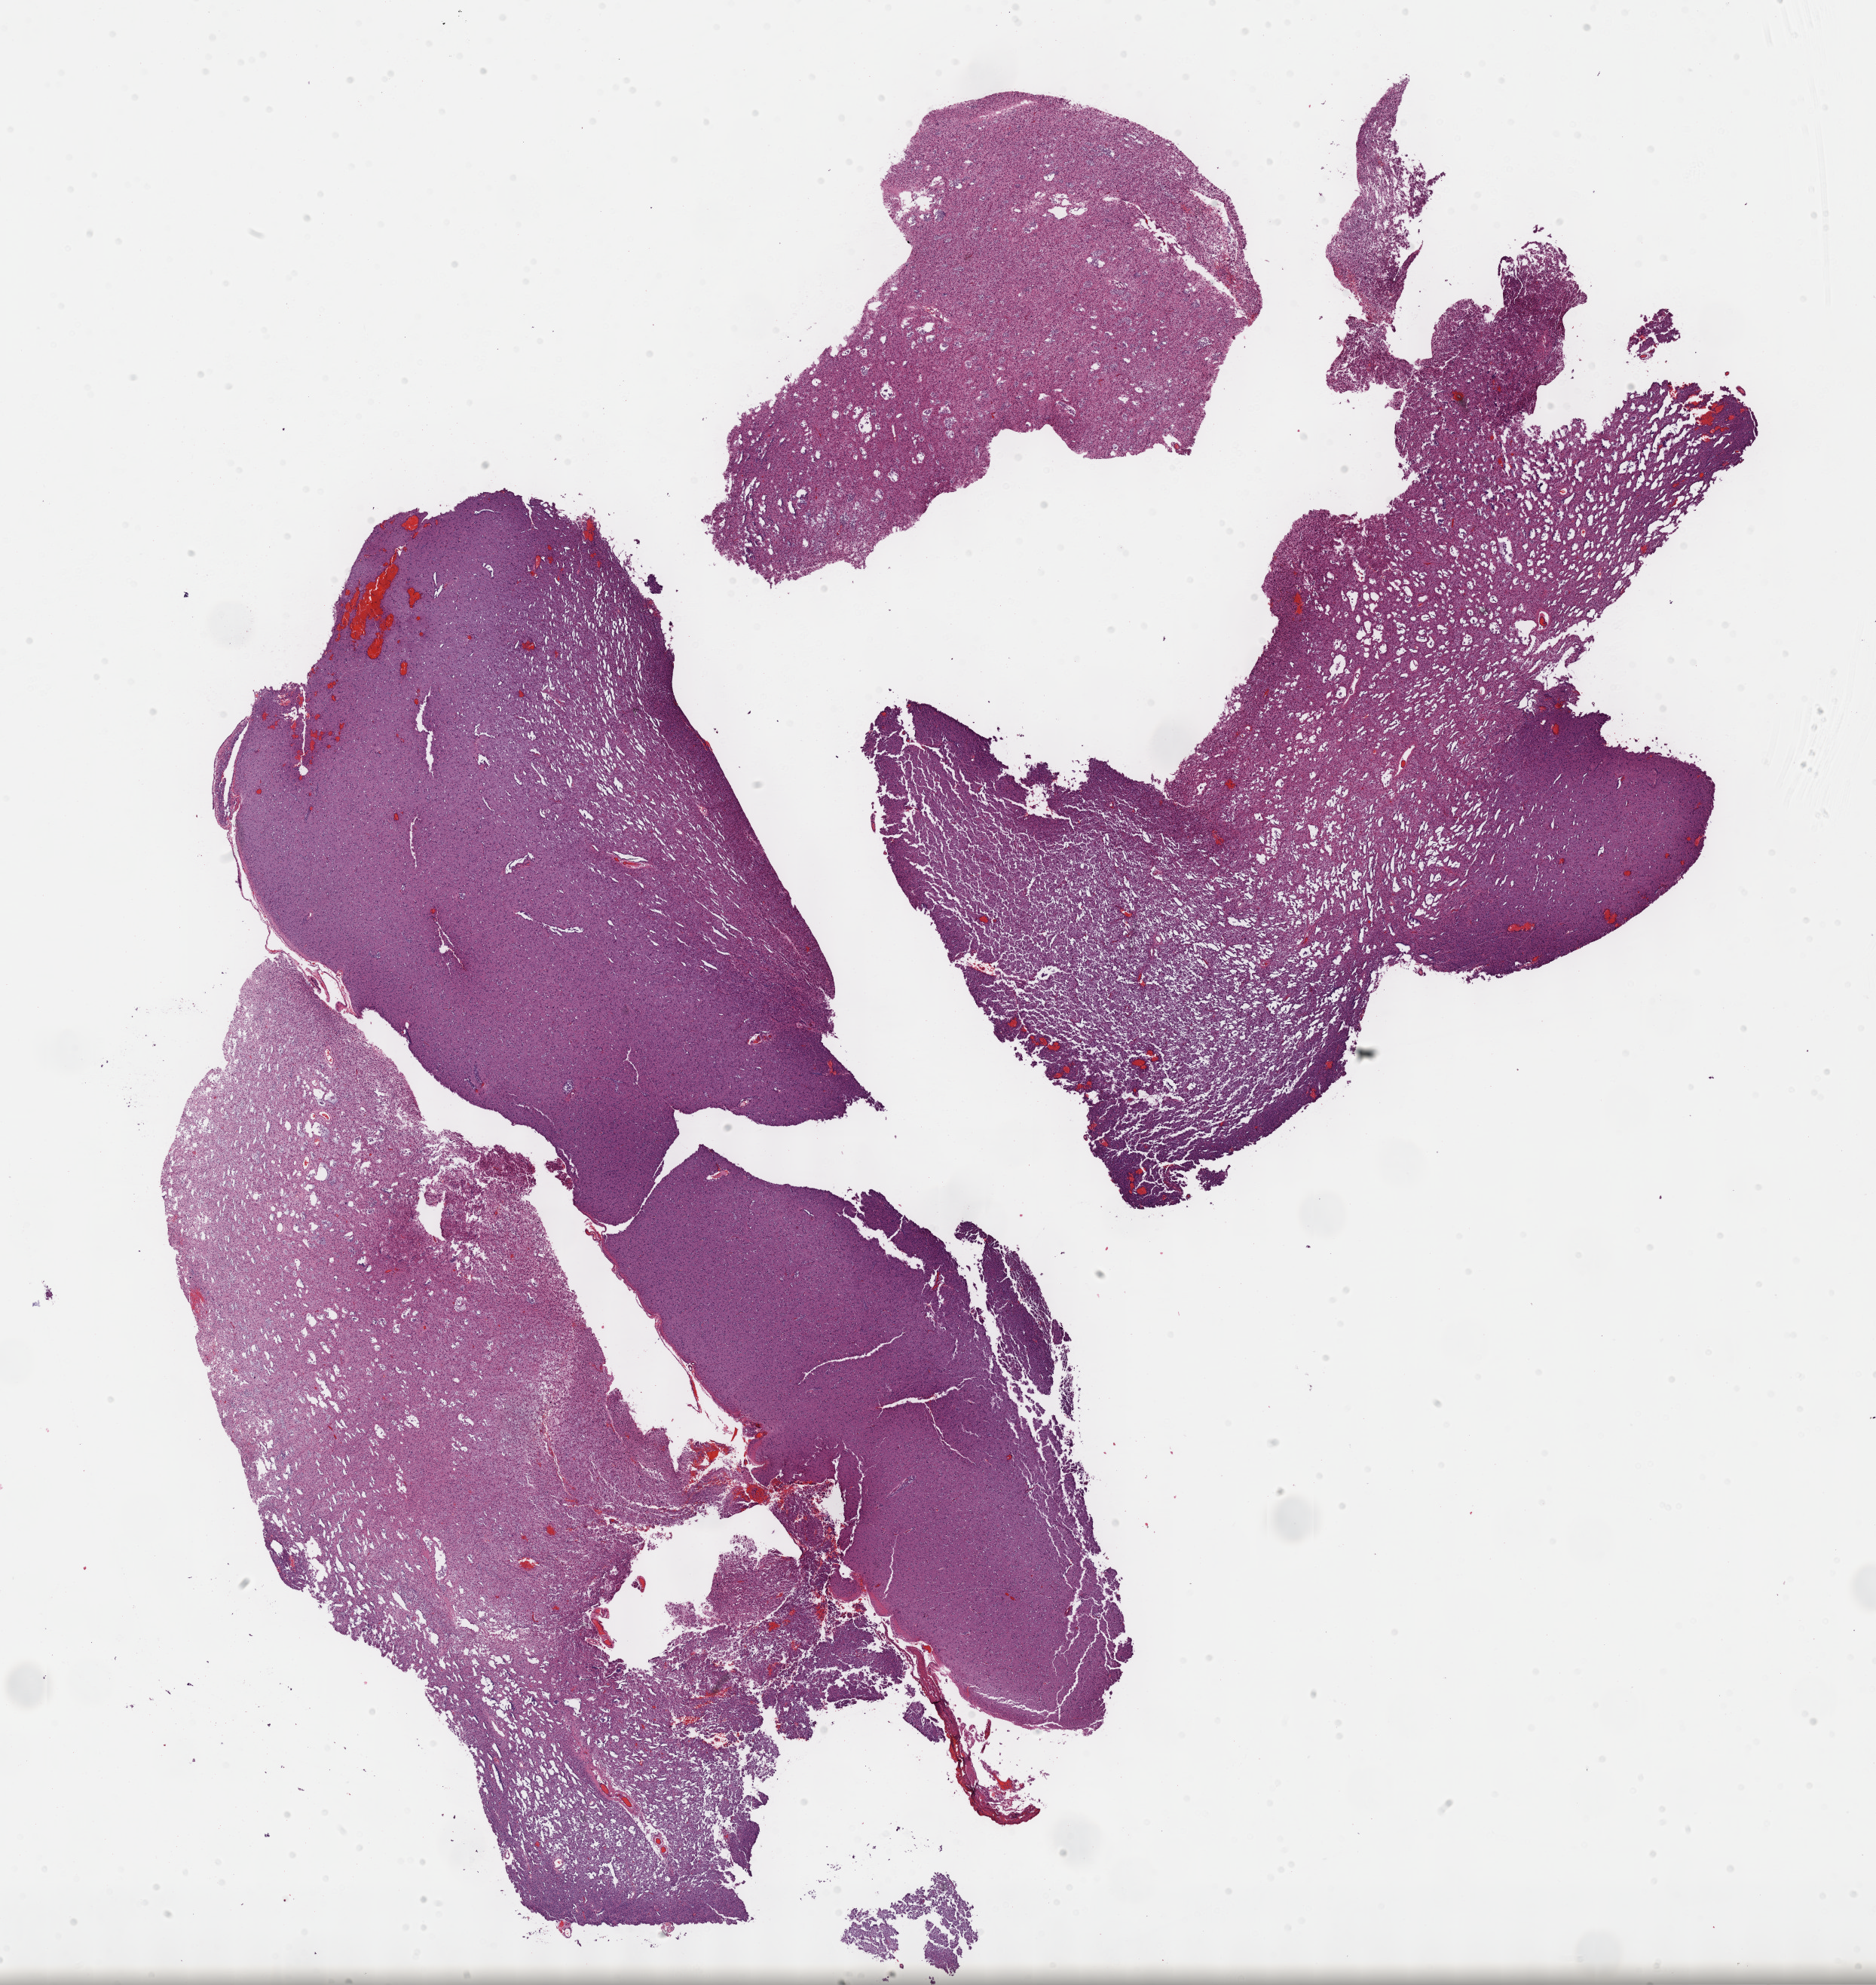
Whole-slide histology image, Hematoxylin and eosin (H&E) stained — whole scanned area (about 20.1 x 21.3 mm, from a 40x scan) shown as a low-resolution overview, formalin-fixed paraffin-embedded (FFPE) diagnostic section, sample: primary tumour, brain. Male patient; age at initial diagnosis 28 years. Histologic grade: G2 (moderately differentiated).
- diagnosis: Mixed glioma